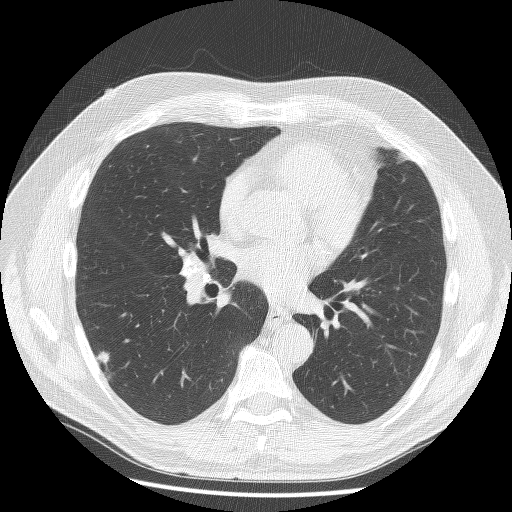
Chest CT (low-dose screening protocol), one axial image; first (baseline) screen; lung window (W 1500 / L -600 HU); lung (sharp) reconstruction kernel (BONE). Male participant, aged 61 years at enrolment.
Expert-annotated lung lesion, bounding box [x1, y1, x2, y2] px = [78, 337, 127, 387]. Screening reader's record for this exam (one nodule recorded; not confirmed to be the boxed lesion): non-calcified nodule or mass ≥4 mm, right lower lobe, 10 × 8 mm, spiculated (stellate) margins, soft tissue attenuation. Participant outcome: lung cancer diagnosed 407 days after this screen (after the second annual screen) — adenosquamous carcinoma, right lower lobe, poorly differentiated (G3), stage IV (AJCC 6th edition), 45 mm at pathology.